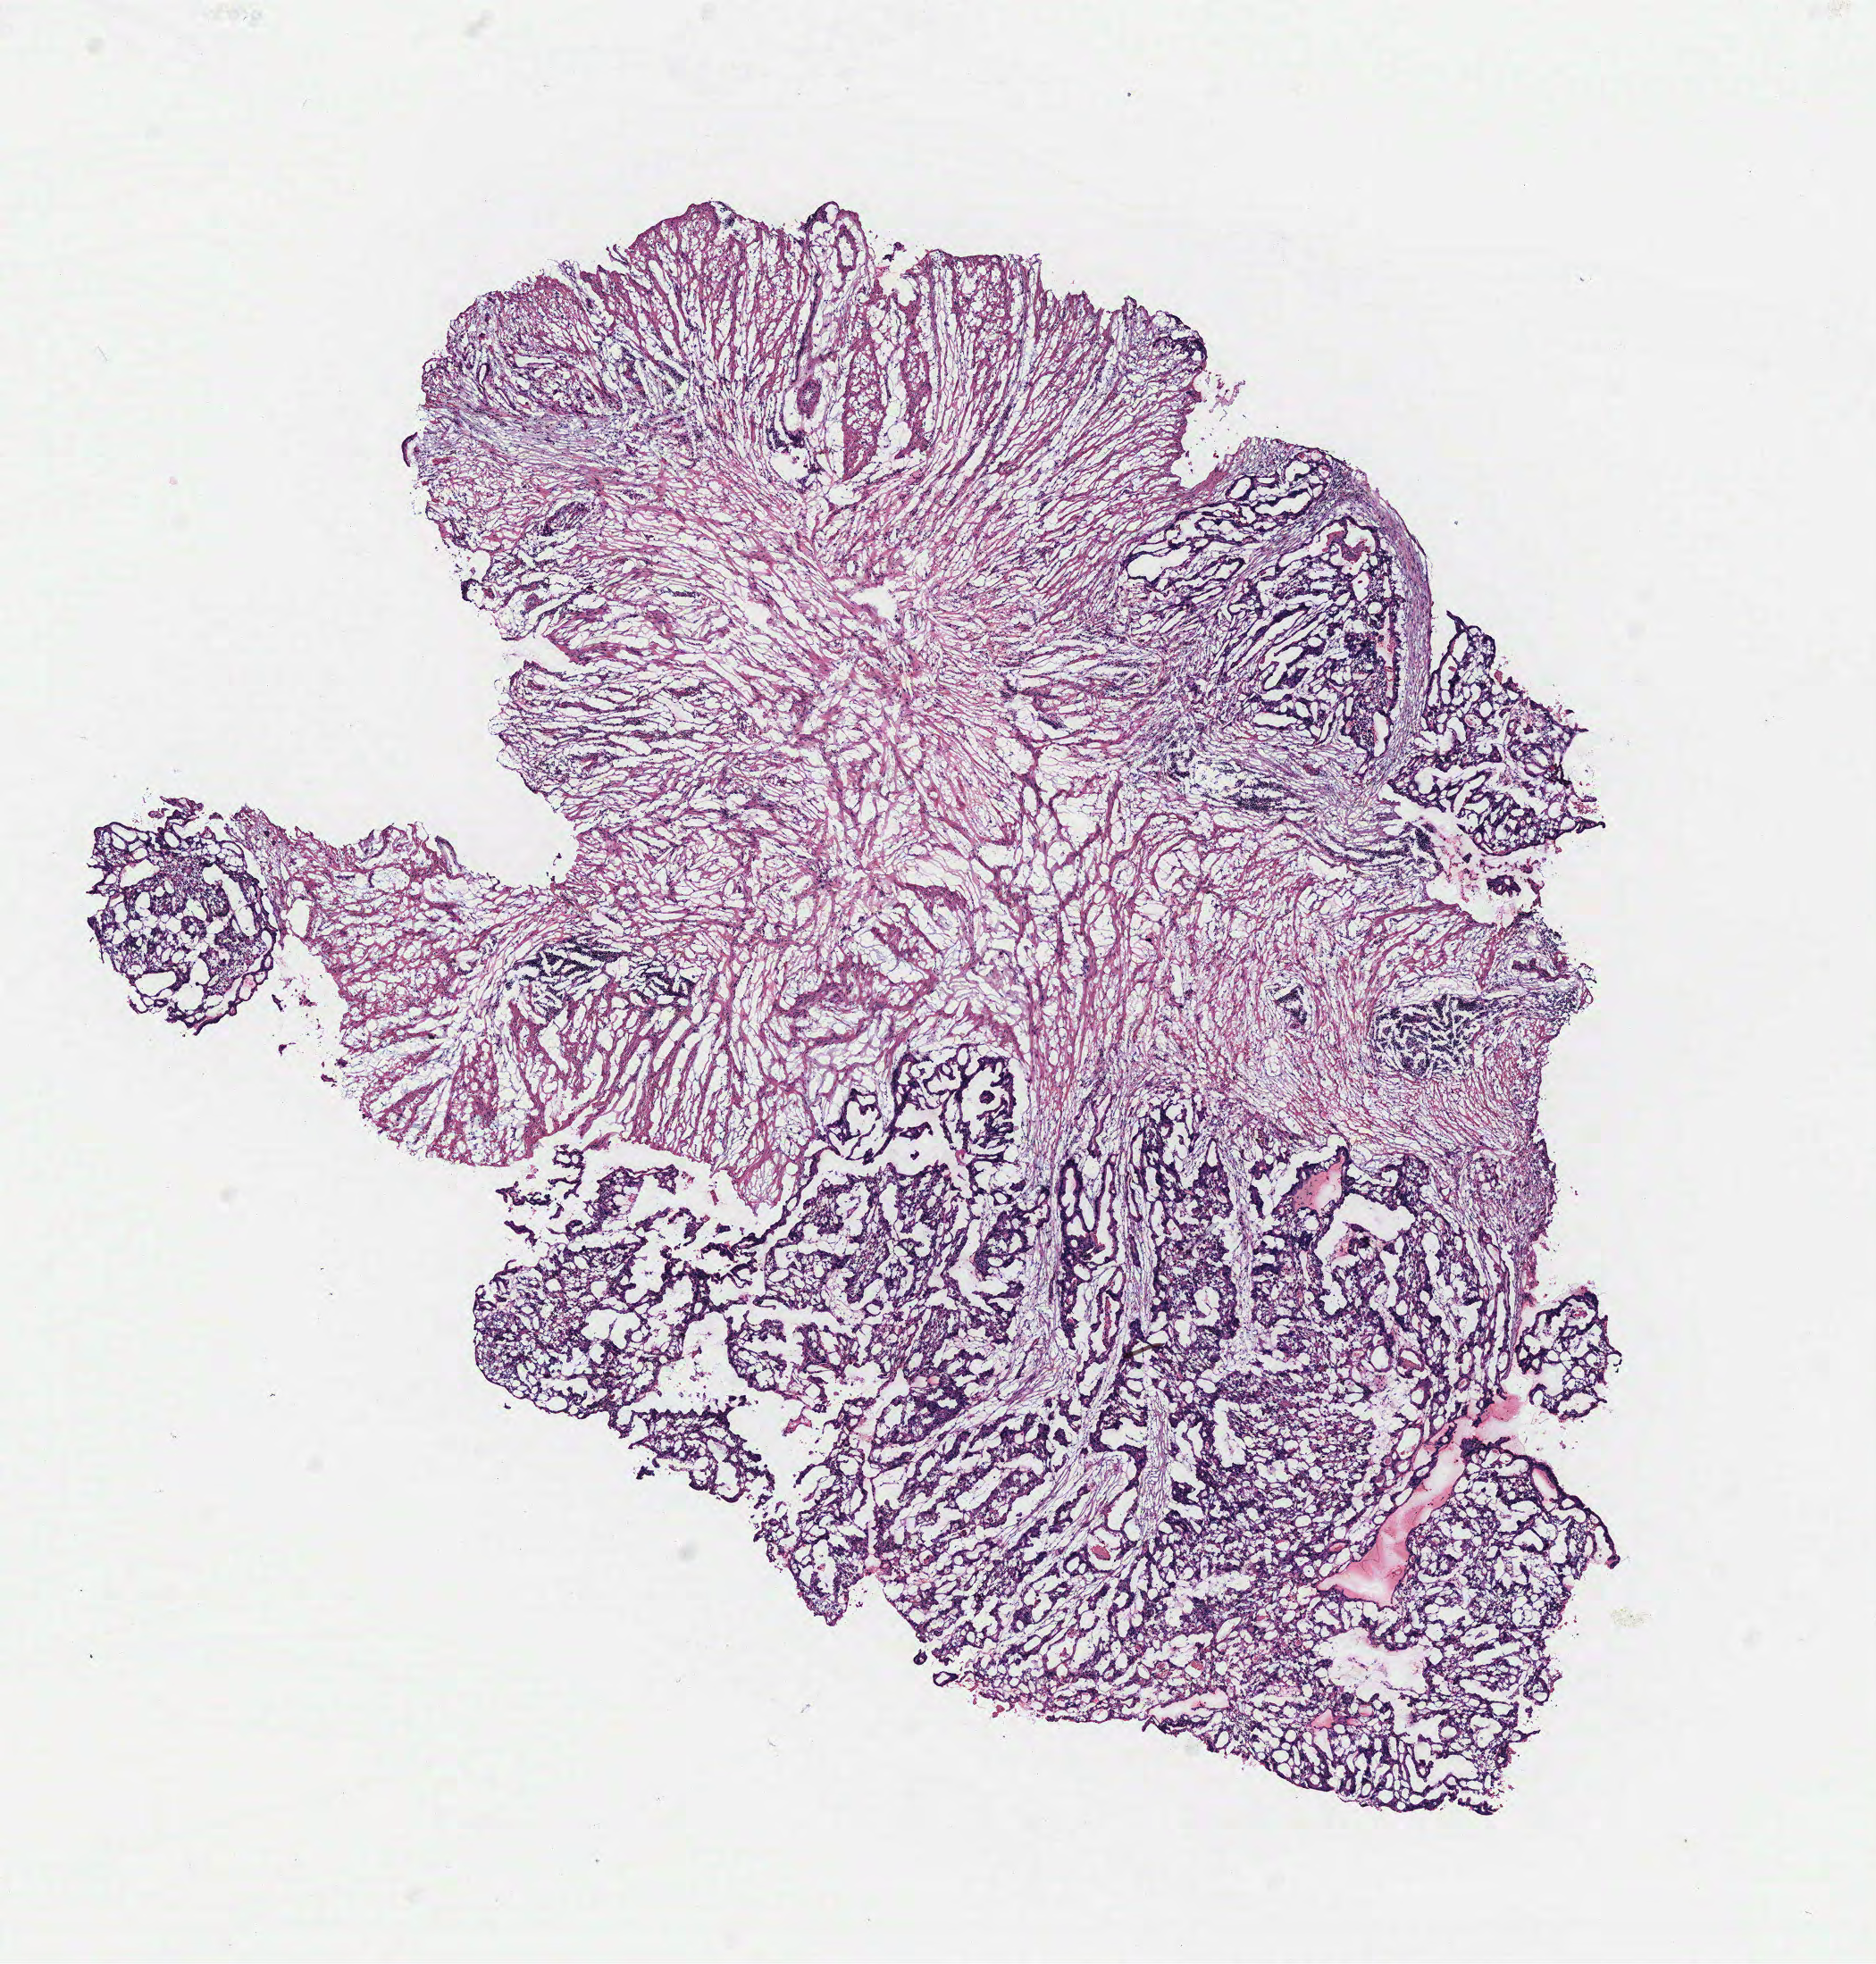
Digitized H&E-stained tissue section (whole slide) — low-resolution overview of the scanned area, about 8.4 x 8.8 mm (acquisition: 40x scan). Tumour tissue sample, colon. Female, 54 y/o.
Primary tumour site (as recorded): colon. AJCC pathologic stage: IIIB. Diagnosis: Adenocarcinoma, NOS.